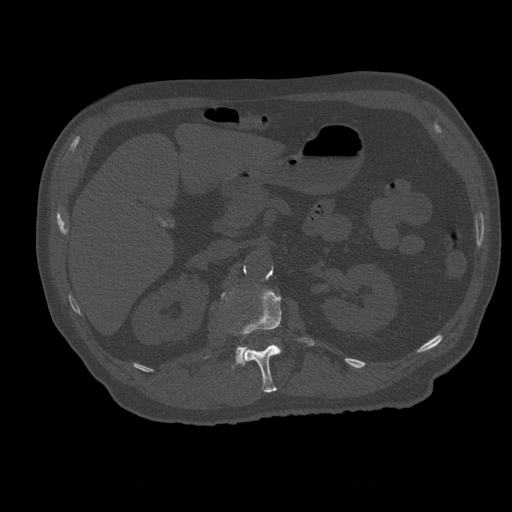
CT including the spine, one axial slice; position 231 of 399 along the scan axis; reconstruction kernel STANDARD; bone window (W 1800 / L 400 HU); 1.25 mm slice thickness; 512 × 512 image matrix. Patient age 73 years. Case-level facts recorded for this patient, not image findings: primary cancer: prostate.
Annotated regions visible in this slice (semi-automatically segmented with operator editing):
- L1 vertebra: bounding box (x1, y1, x2, y2) in pixels: (239, 290, 315, 393)
- L2 vertebra: (222, 293, 247, 368)